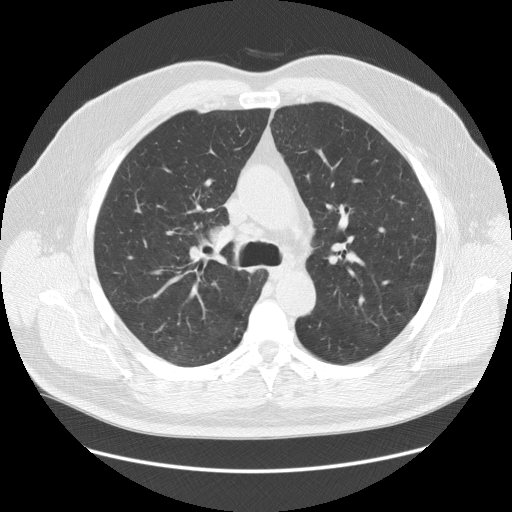
Low-dose screening chest CT, axial slice, first (baseline) screen, lung window (W 1500 / L -600 HU), 2.5 mm slice thickness, standard (soft-tissue) reconstruction kernel (STANDARD), slice 47 of 140 in the series. Male participant, aged 64 years at enrolment.
Lesion marked by an expert reader, bounding box [x1, y1, x2, y2] px = [178, 209, 253, 275]. Reader record for this screening exam (exam-level; its link to the box is not recorded): non-calcified nodule or mass ≥4 mm, right lower lobe, 7 × 5 mm, smooth margins, soft tissue attenuation. Later outcome: lung cancer diagnosed 456 days after this screen — adenocarcinoma, NOS, right upper lobe, poorly differentiated (G3), stage IB (AJCC 6th edition), 37 mm at pathology.